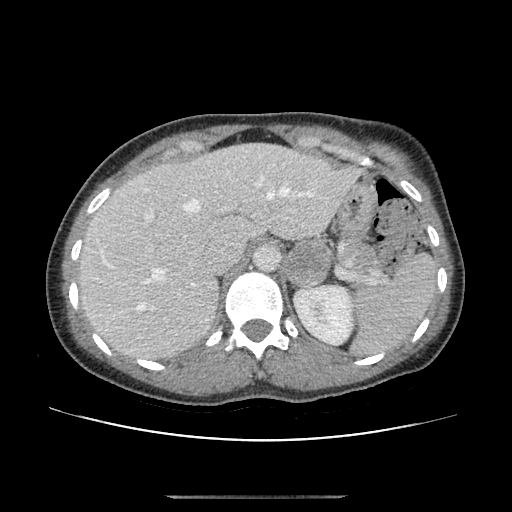
Contrast-enhanced abdominal CT, one axial slice. Position 76 of 179 along the scan axis. 120 kVp. Soft-tissue window (W 400 / L 40 HU). 2.5 mm slice thickness. 512 × 512 image matrix, field of view 360 × 360 mm. Patient: female, 51 years. Case-level facts recorded for this patient, not image findings: diagnosis: adrenocortical carcinoma; tumour side: left adrenal; tumour size at pathology: 3.5 cm; Ki-67 index: 45 %; stage (as recorded): 1.
Structures marked on this image (semi-automatically segmented with operator editing):
- mass: bounding box <287,241,330,286> (left, top, right, bottom; pixels)